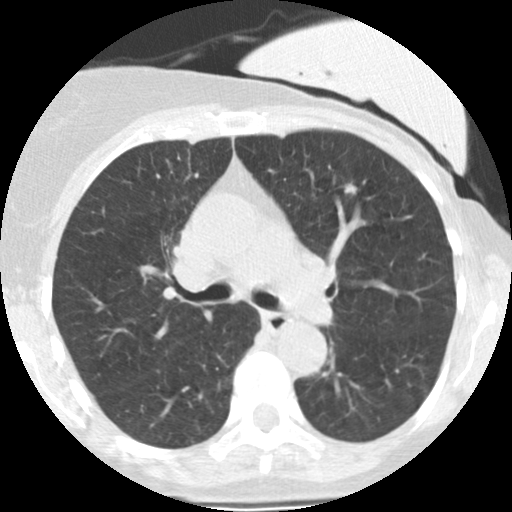
Low-dose screening chest CT, axial slice; second annual screen; lung window (W 1500 / L -600 HU); standard (soft-tissue) reconstruction kernel (STANDARD); slice 94 of 251 in the series. Female participant, aged 66 years at enrolment. Former smoker at enrolment.
Expert-annotated lung lesion, bounding box <343,181,360,201> (left, top, right, bottom; pixels). Screening reader's record for this exam (one nodule recorded; not confirmed to be the boxed lesion): non-calcified nodule or mass ≥4 mm, left upper lobe, 7 × 5 mm, smooth margins, soft tissue attenuation, pre-existing on the prior screen: yes; interval growth: yes. Official screen result: positive, change unspecified: nodule(s) >= 4 mm or enlarging nodule(s), mass(es), or other non-specific abnormalities suspicious for lung cancer. Participant outcome: lung cancer diagnosed 218 days after this screen — adenocarcinoma, NOS, left lower lobe, poorly differentiated (G3), stage IA (AJCC 6th edition), 8 mm at pathology.